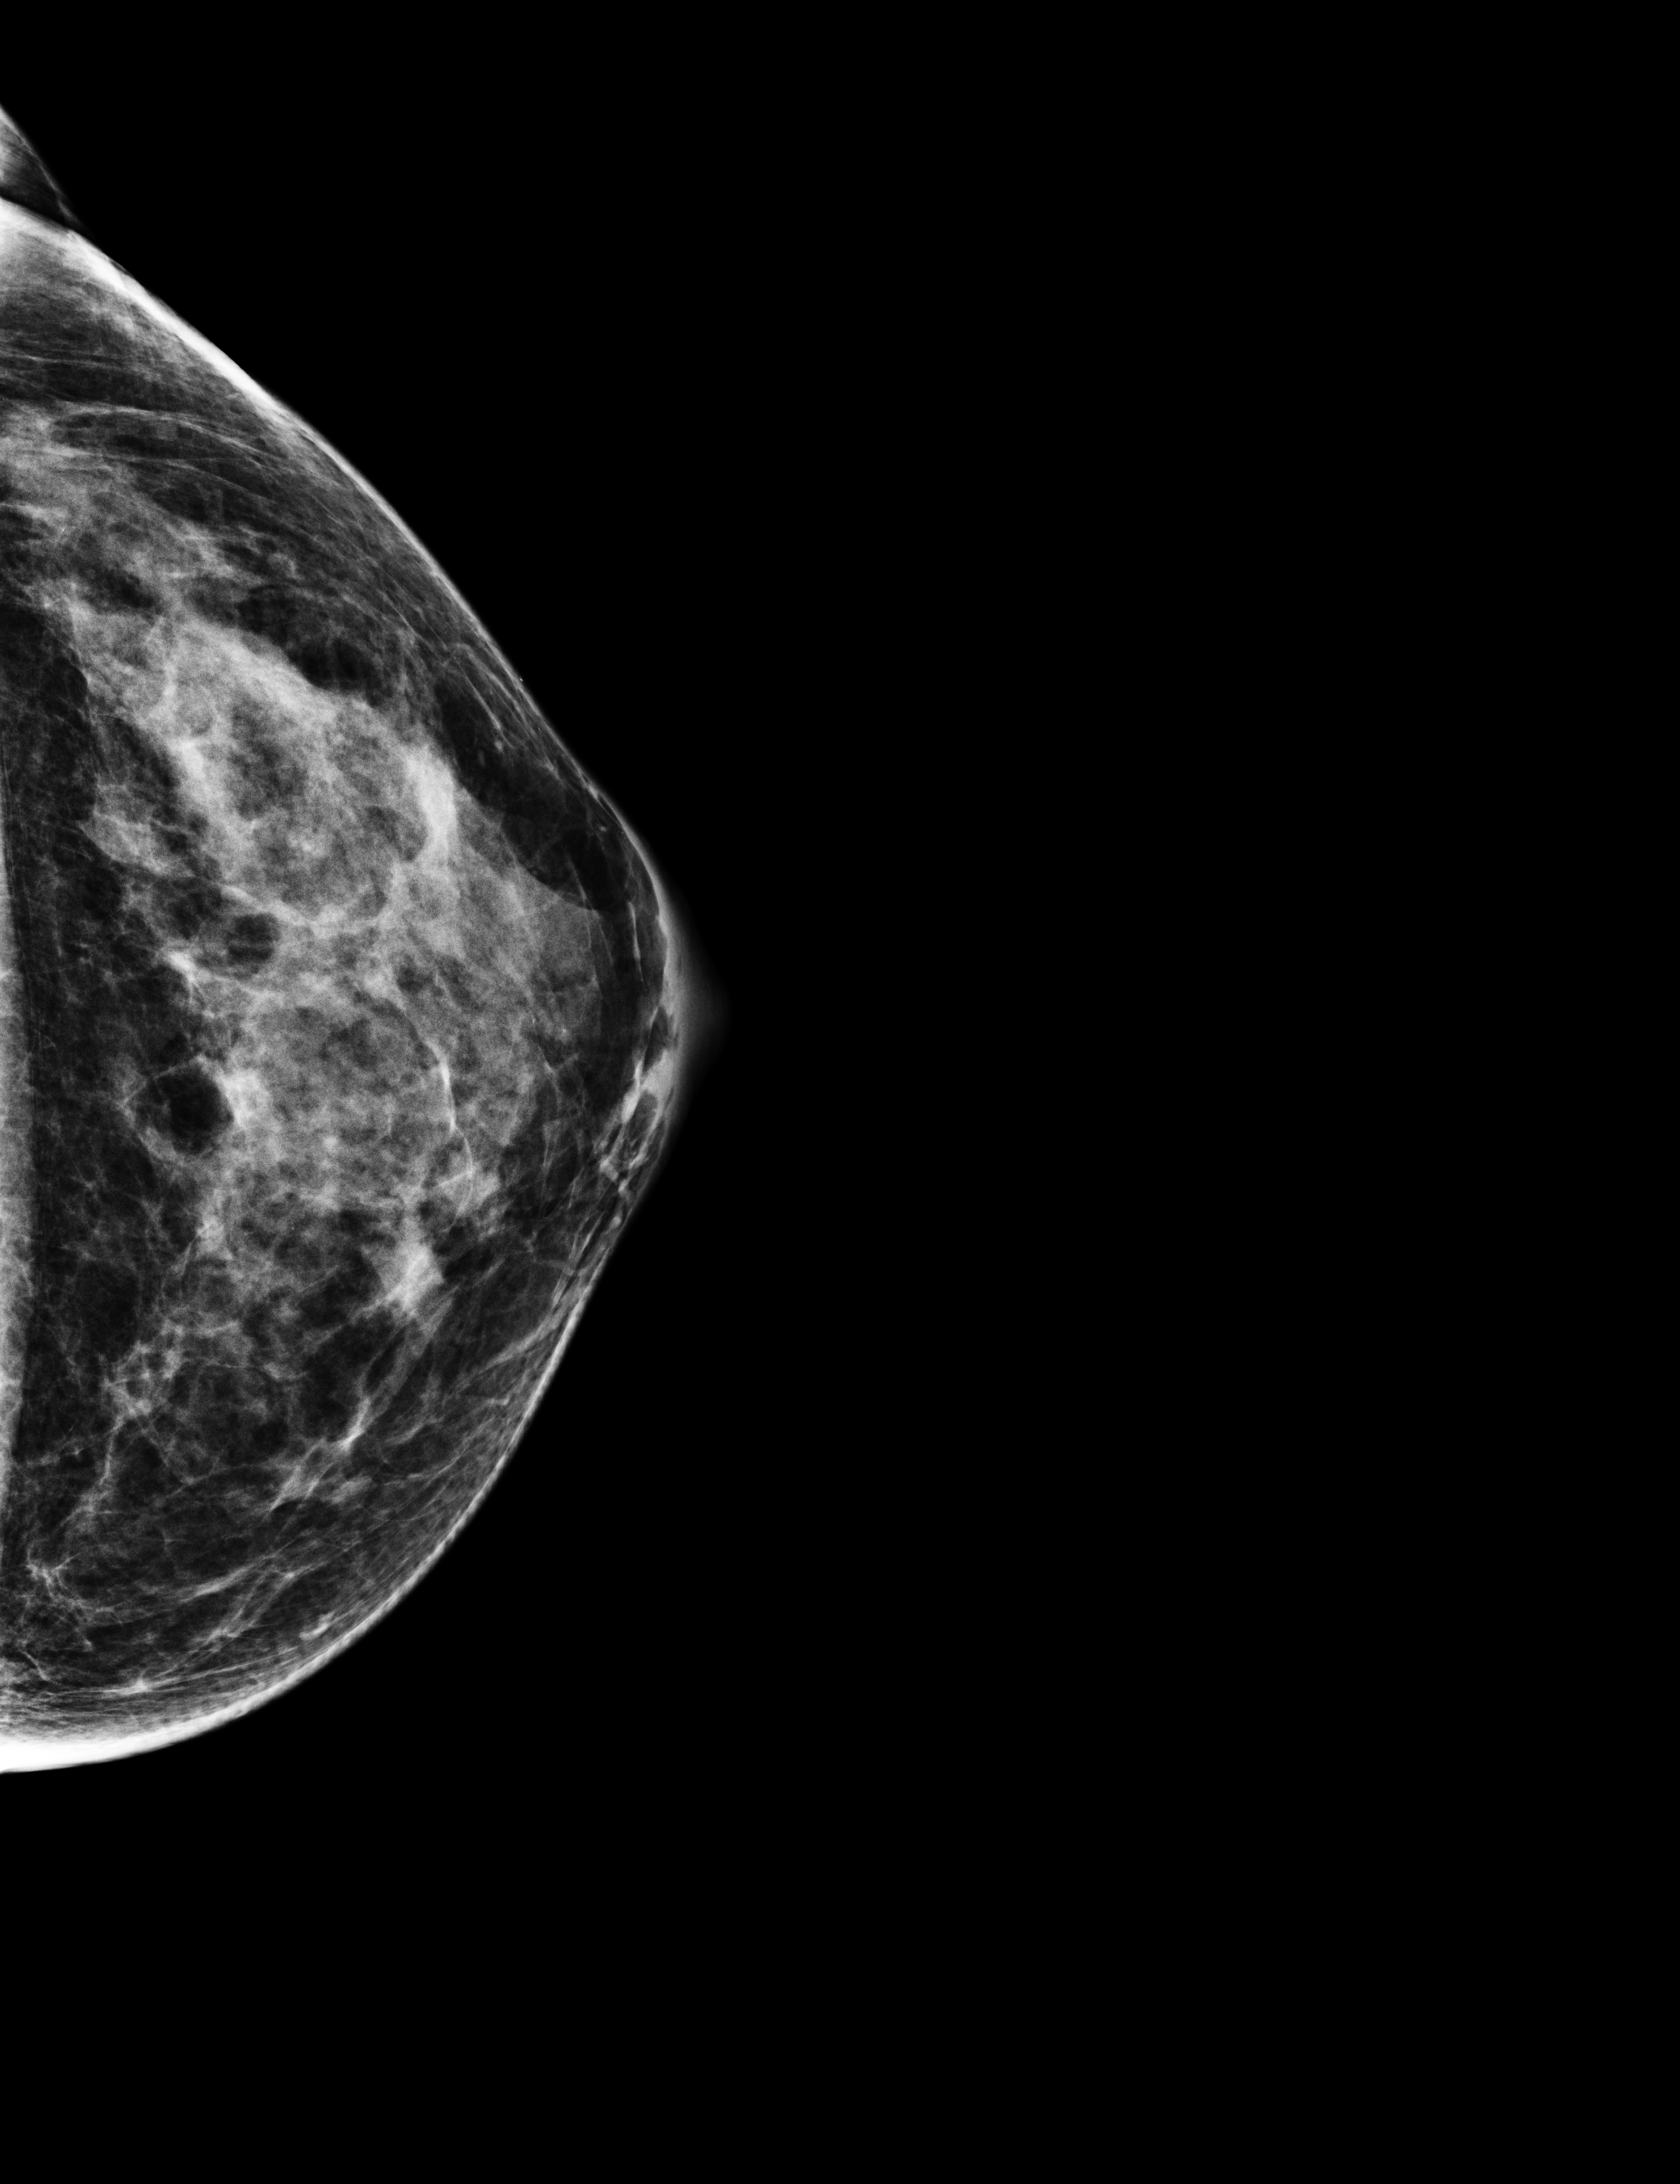
Annual screening mammography examination.
Image type: full-field digital mammogram. Breast: left. Projection: cranio-caudal projection.